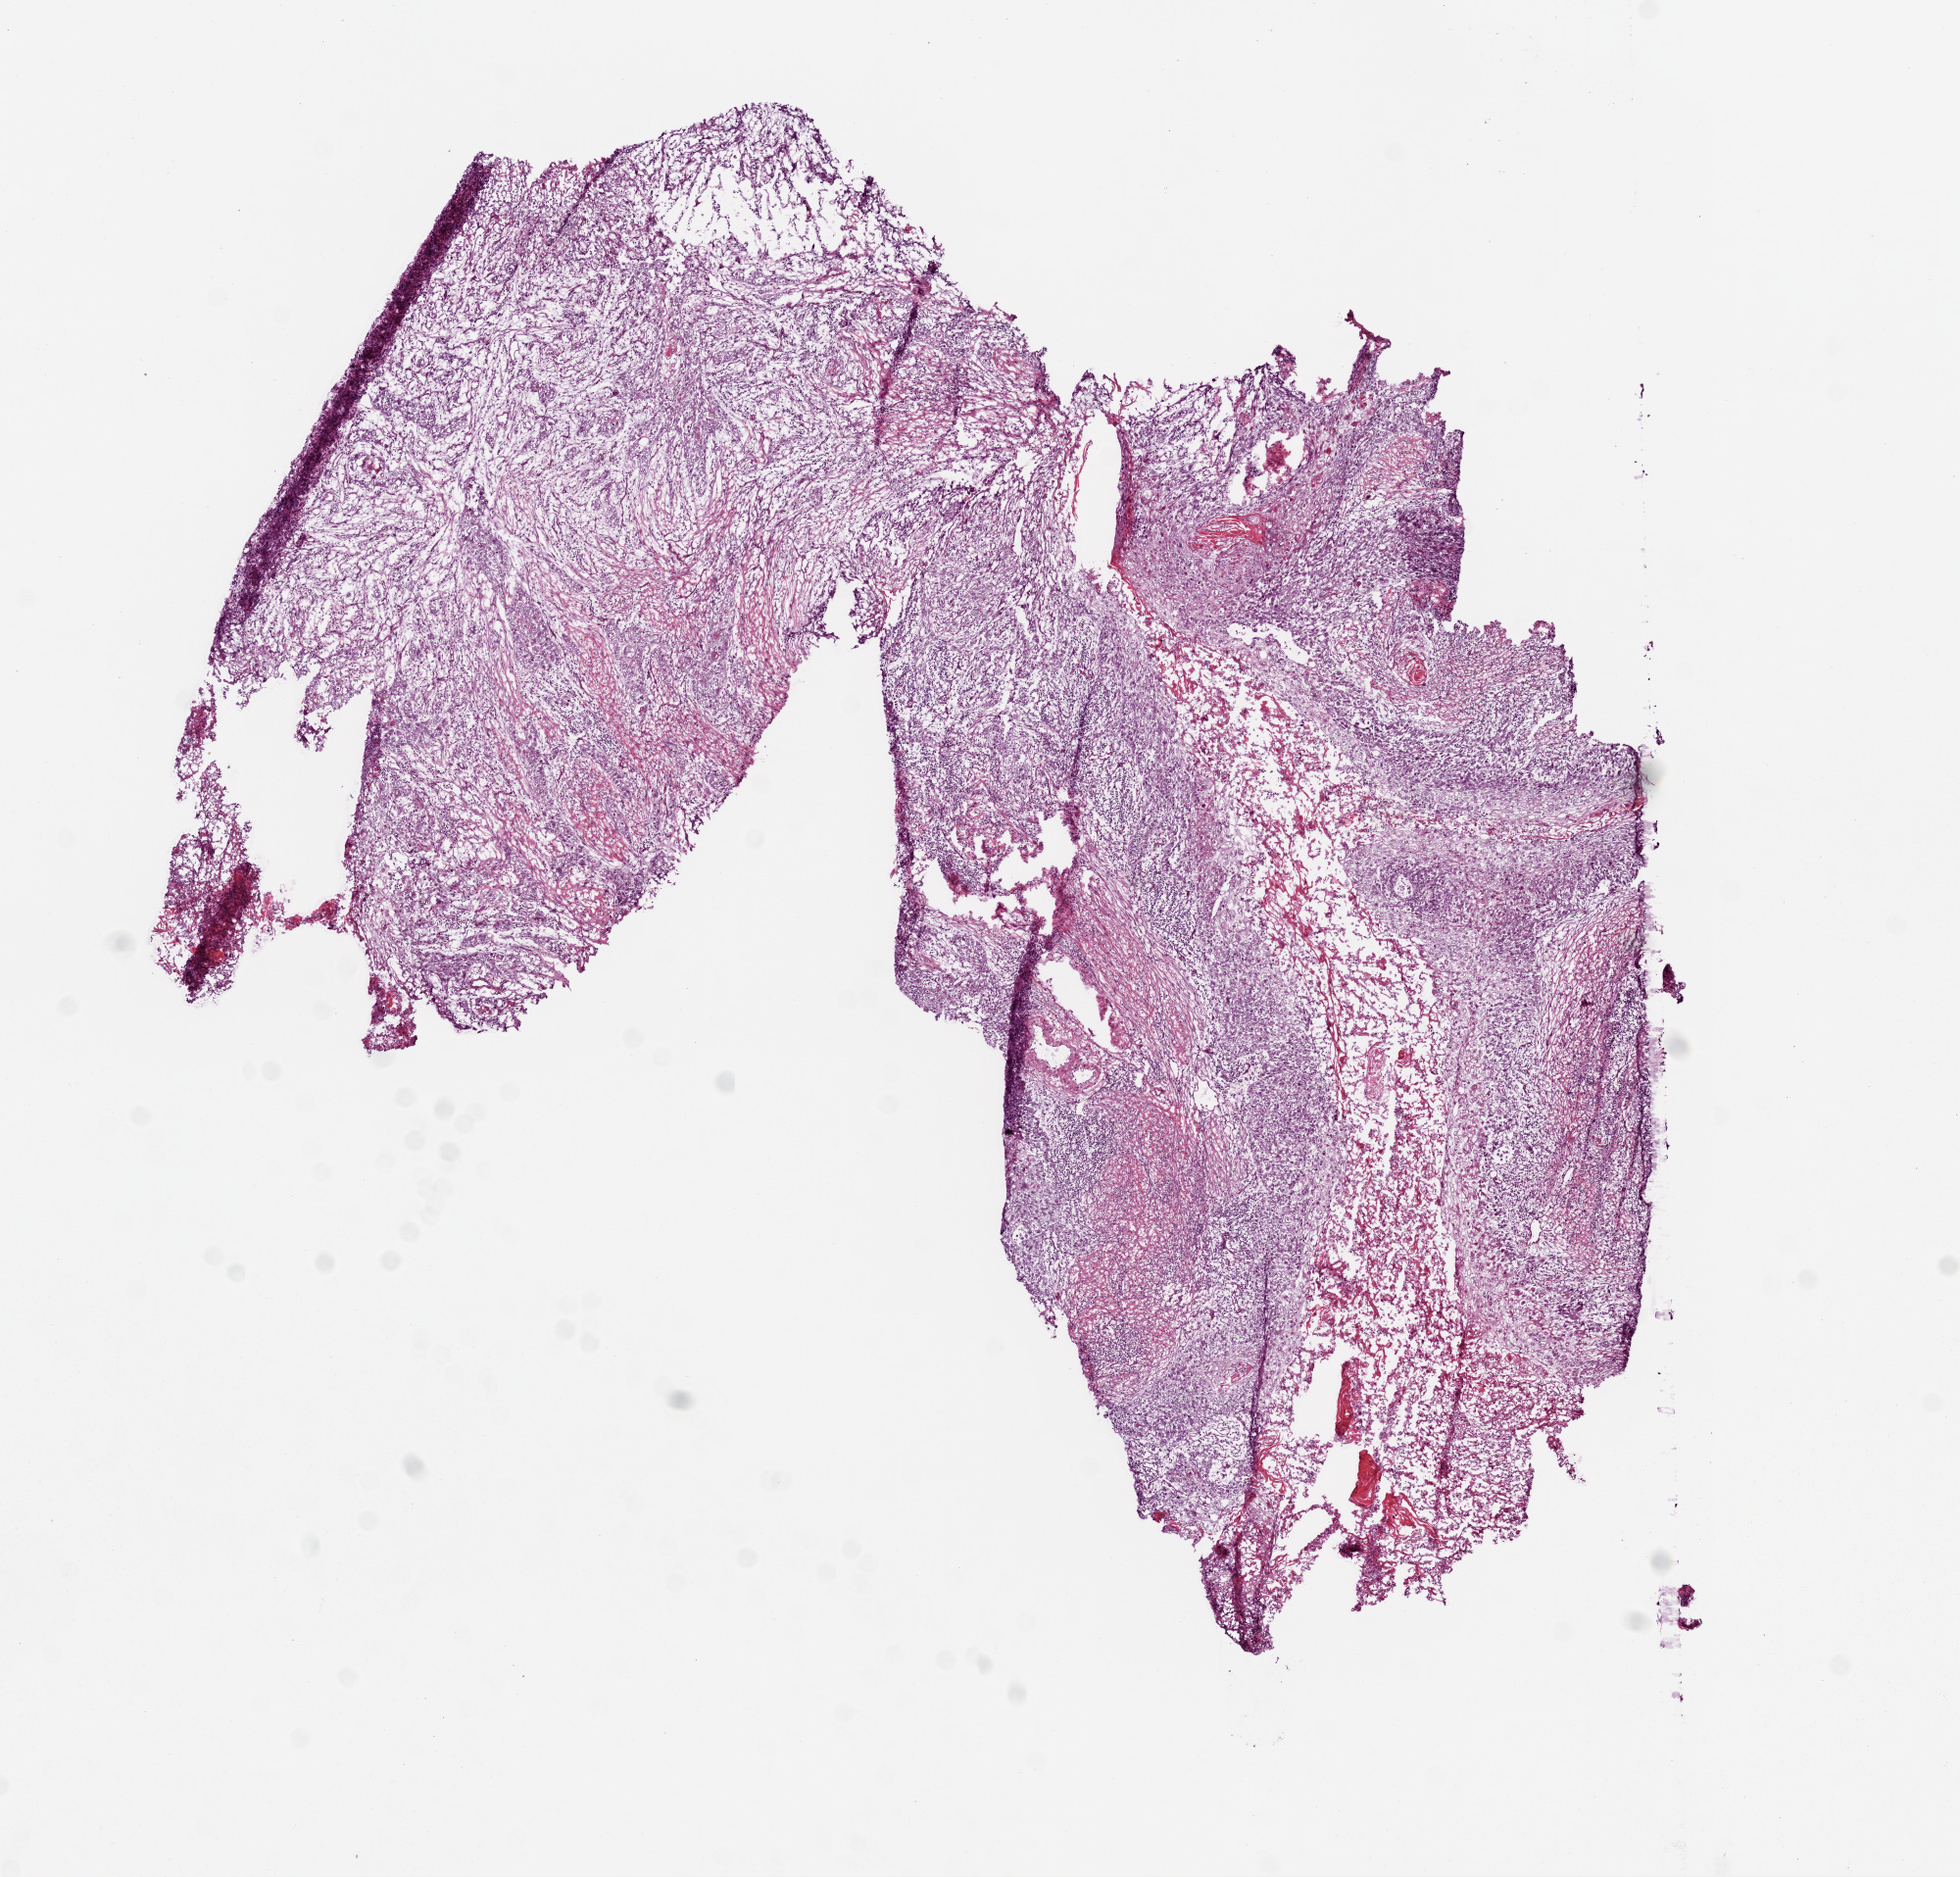
Digitized H&E-stained tissue section (whole slide), whole scanned area (about 8.0 x 7.7 mm, acquisition: 20x scan) shown as a low-resolution overview; frozen section; primary tumour sample from the head and neck. Male patient; age at initial diagnosis 59 years.
Diagnosis: Squamous cell carcinoma, NOS (floor of mouth, NOS).